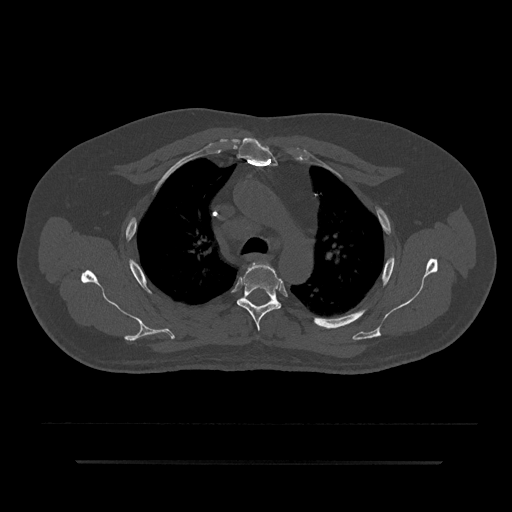
CT including the spine, one axial slice. Slice 616 of 797 in the series (ordered by position). 120 kVp. Bone window (W 1800 / L 400 HU). 0.5 mm slice thickness. 512 × 512 image matrix. Patient: male, 59 years. From the clinical record (not read from this slice): primary cancer: bile ducts.
Structures marked on this image (semi-automatic segmentation, software-assisted and operator-edited):
- T3 vertebra: bounding box (x1, y1, x2, y2) in pixels: (266, 264, 272, 268)
- T4 vertebra: (235, 262, 283, 331)
- T5 vertebra: (238, 298, 278, 303)